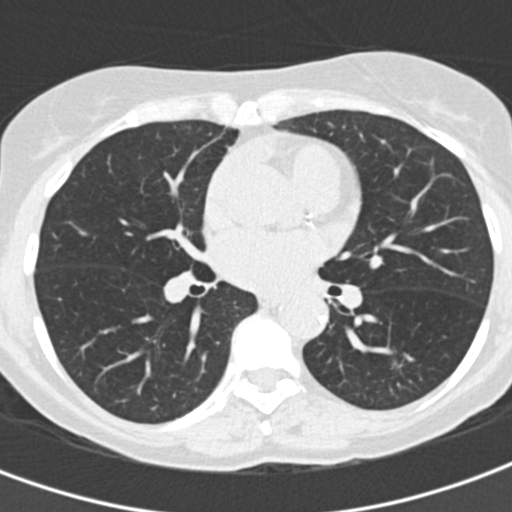
Low-dose screening chest CT, one axial slice; slice 79 of 155 in the series (ordered by position); reconstruction kernel B30f; 120 kVp; lung window (W 1500 / L -600 HU); 2 mm slice thickness; 512 × 512 image matrix, field of view 282 × 282 mm.
Annotated regions visible in this slice (manually delineated by an expert):
- lesion 1 (tumor, lower lobe of left lung): bounding box (x1, y1, x2, y2) in pixels: (390, 359, 402, 371)